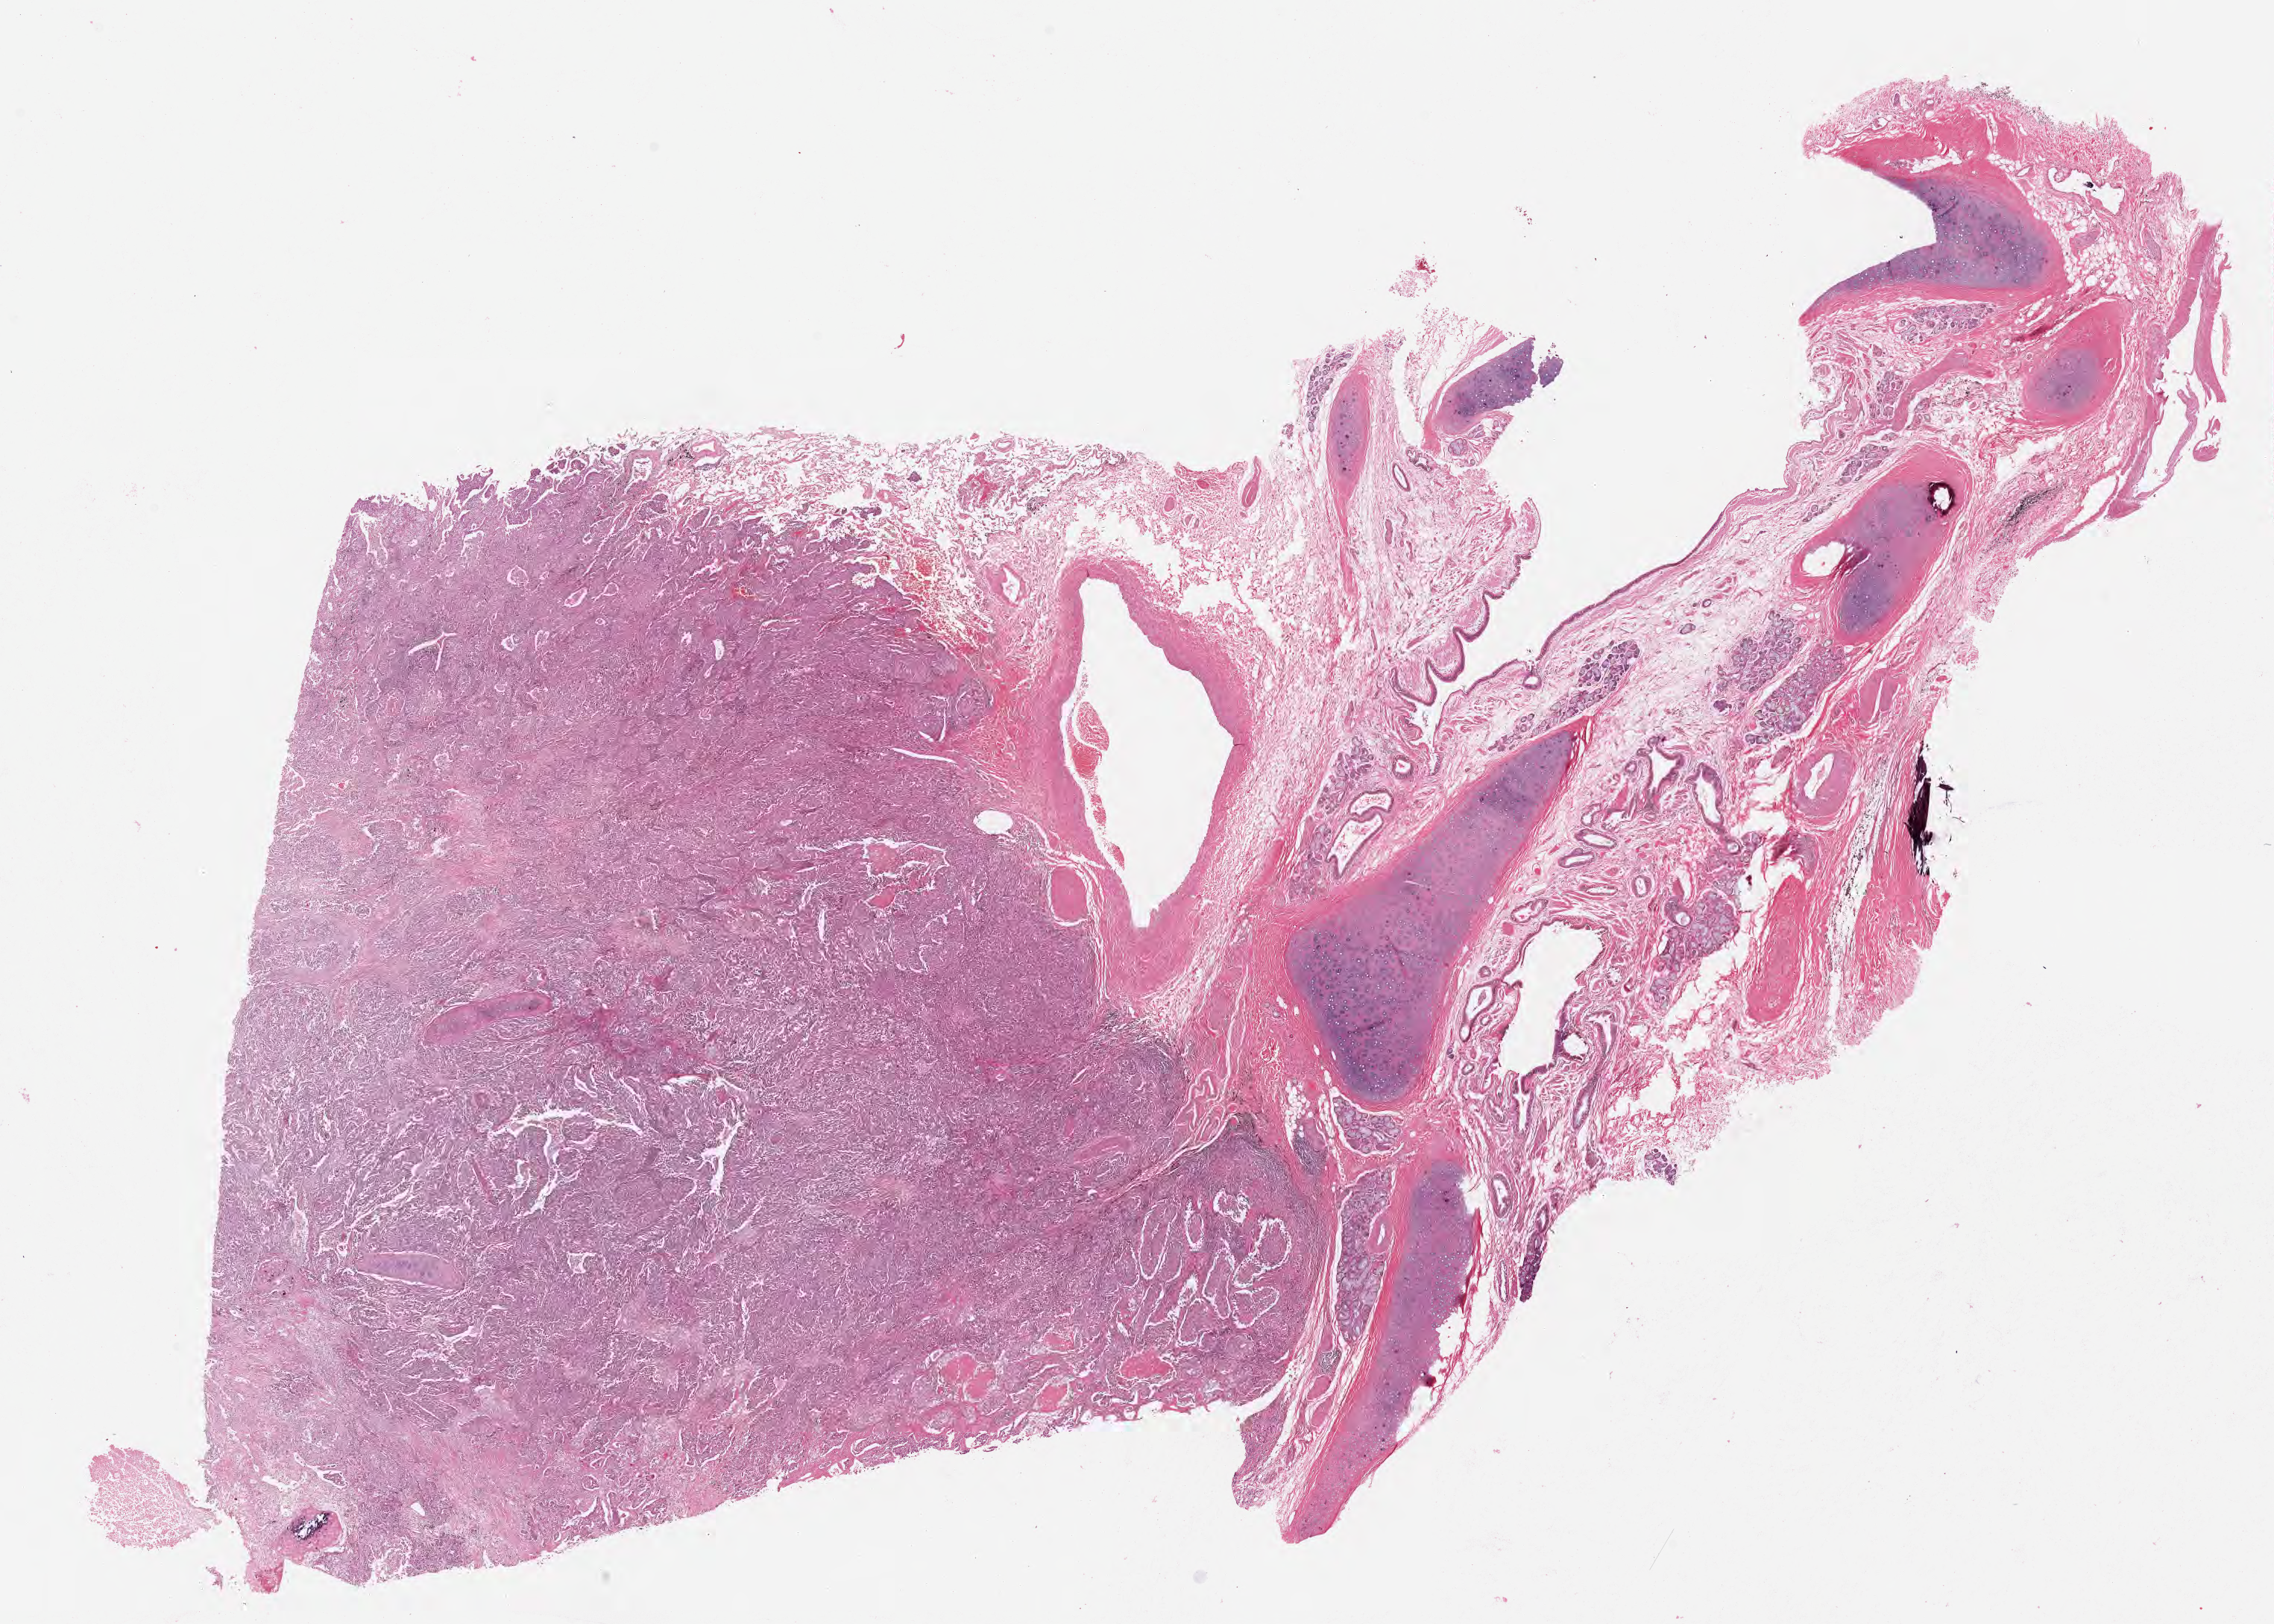
Haematoxylin and eosin whole-slide image, whole scanned area (about 24.6 x 17.6 mm) shown as a low-resolution overview, FFPE section, specimen: primary tumor, site: upper lobe of left lung. Male patient, aged 75. Composition of this section per pathologist review: tumor cells 60%, tumor nuclei 70%, stromal cells 5%, necrosis 5%, normal cells 30%. Inflammatory infiltration, as recorded: lymphocyte infiltration 4%, monocyte infiltration 1%, neutrophil infiltration 2%.
* histologic diagnosis: Adenocarcinoma, NOS
* AJCC pathologic stage: Stage IB